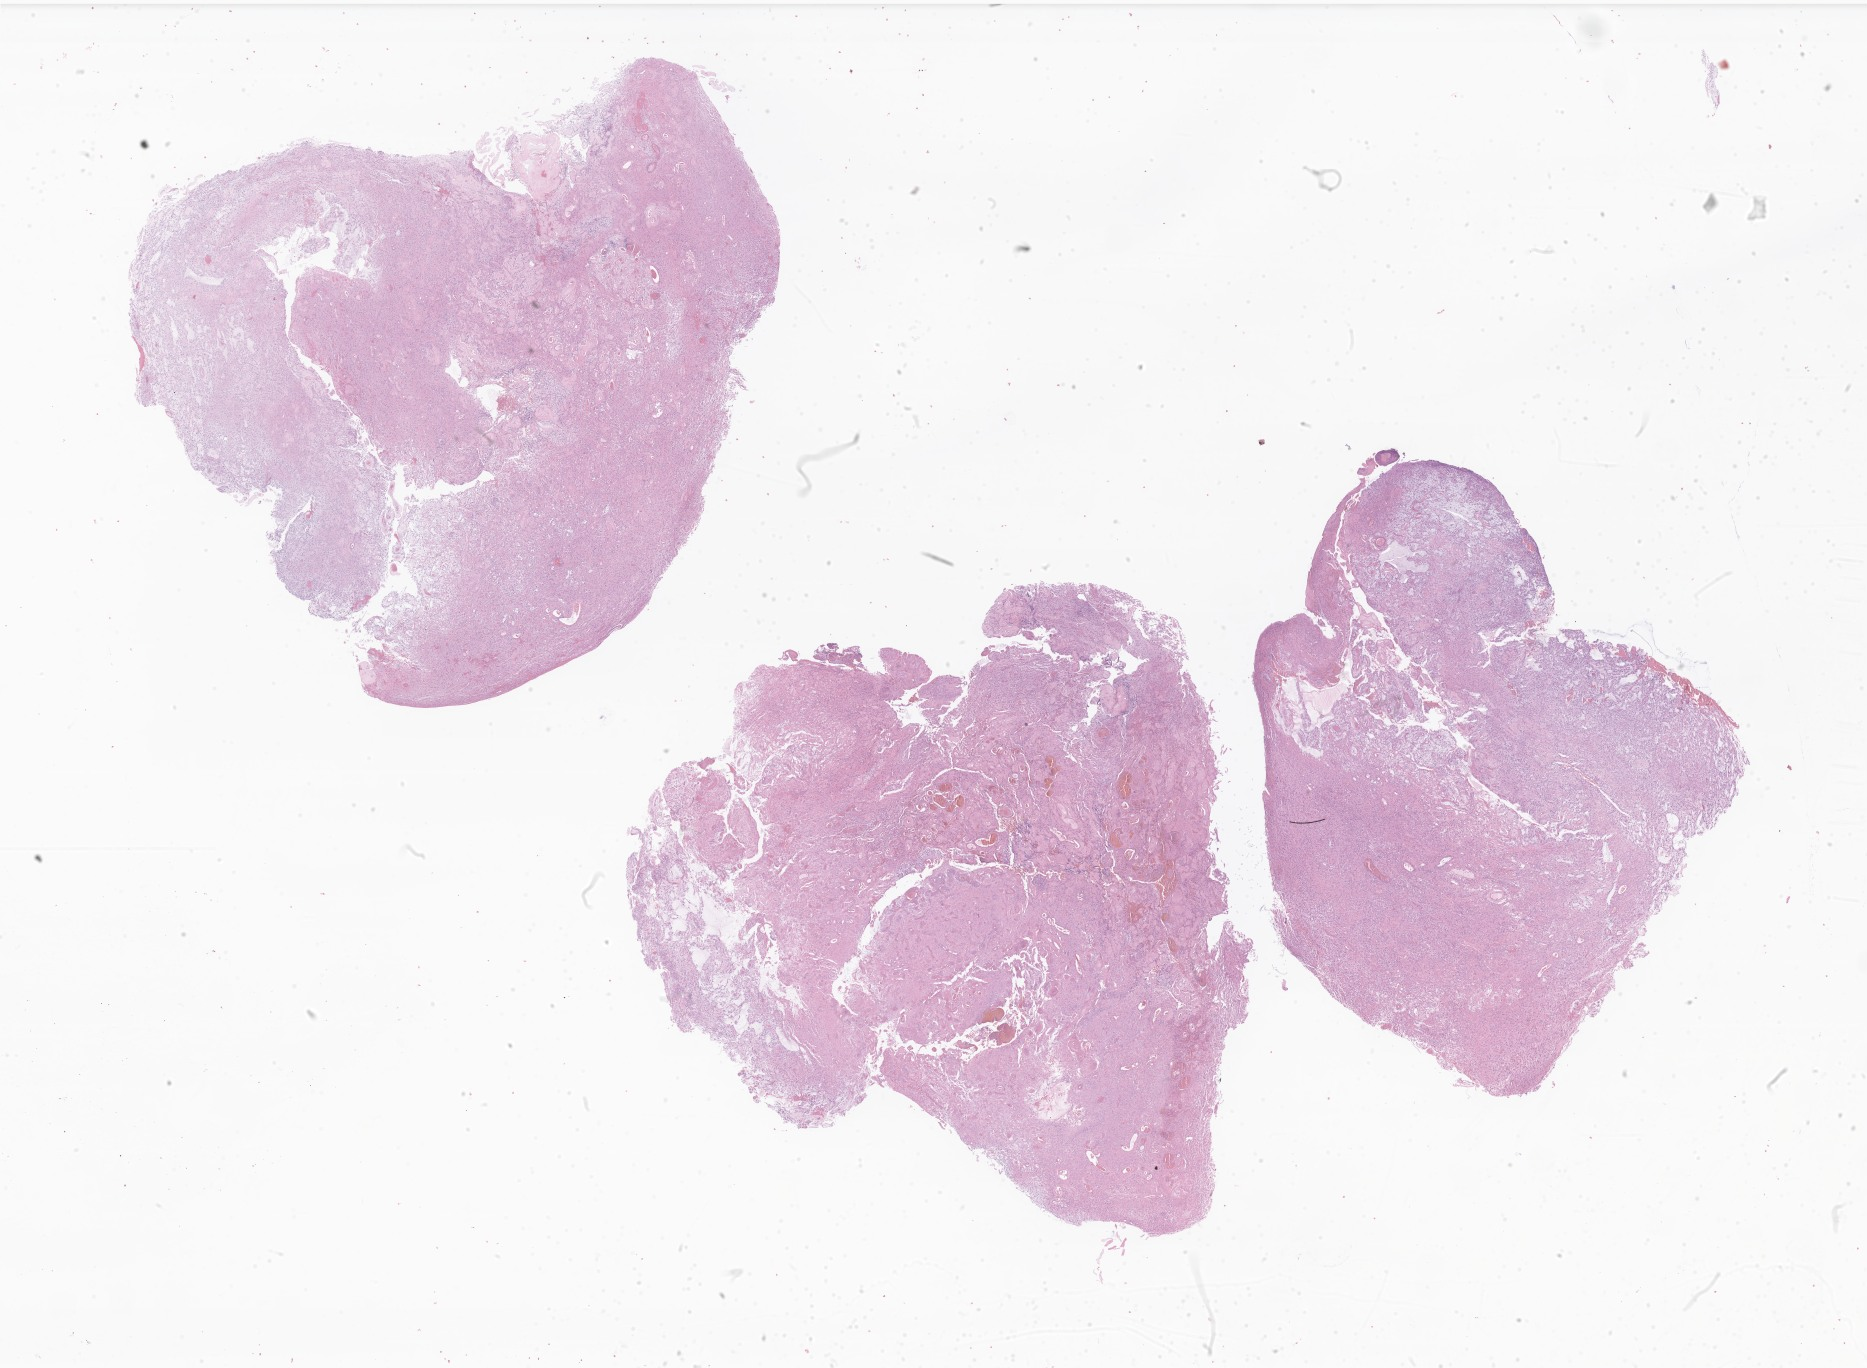
Digitized haematoxylin and eosin-stained section of tumor tissue from the brain, whole scanned area (about 31.5 x 23.1 mm) shown as a low-resolution overview. FFPE section. Female patient, age 171 months (14 years 3 months).
* diagnosis (ICD-O-3 morphology term): Neoplasm, uncertain whether benign or malignant